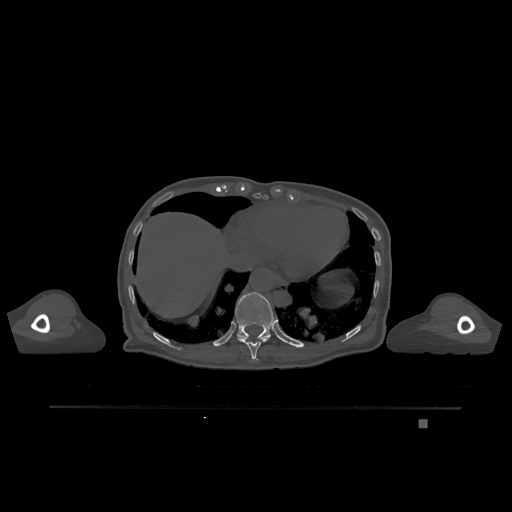
CT including the spine, one axial slice; position 615 of 1317 along the scan axis; bone window (W 1800 / L 400 HU); 0.5 mm slice thickness; 512 × 512 image matrix. Female patient, age 74 years. Case-level facts recorded for this patient, not image findings: primary cancer: lung; vertebrae with lytic lesions (as recorded): T1, T4, T5, T6, L4, L5.
Annotated regions visible in this slice (semi-automatically segmented with operator editing):
- T10 vertebra: bounding box (x1, y1, x2, y2) in pixels: (237, 337, 270, 361)
- T11 vertebra: (229, 292, 276, 340)